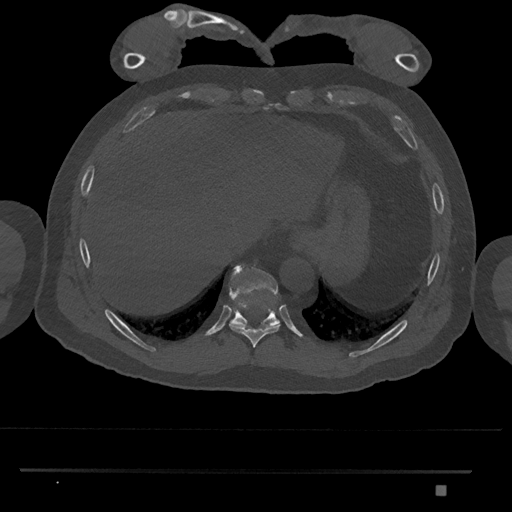
CT including the spine, one axial slice; slice 1033 of 1134 in the series (ordered by position); 120 kVp; bone window (W 1800 / L 400 HU); 0.5 mm slice thickness; 512 × 512 image matrix. Male patient, age 65 years. From the clinical record (not read from this slice): primary cancer: prostate.
Annotated regions visible in this slice (semi-automatically segmented with operator editing):
- T10 vertebra: bounding box [x1, y1, x2, y2] px = [229, 265, 280, 328]
- T9 vertebra: [229, 308, 280, 348]